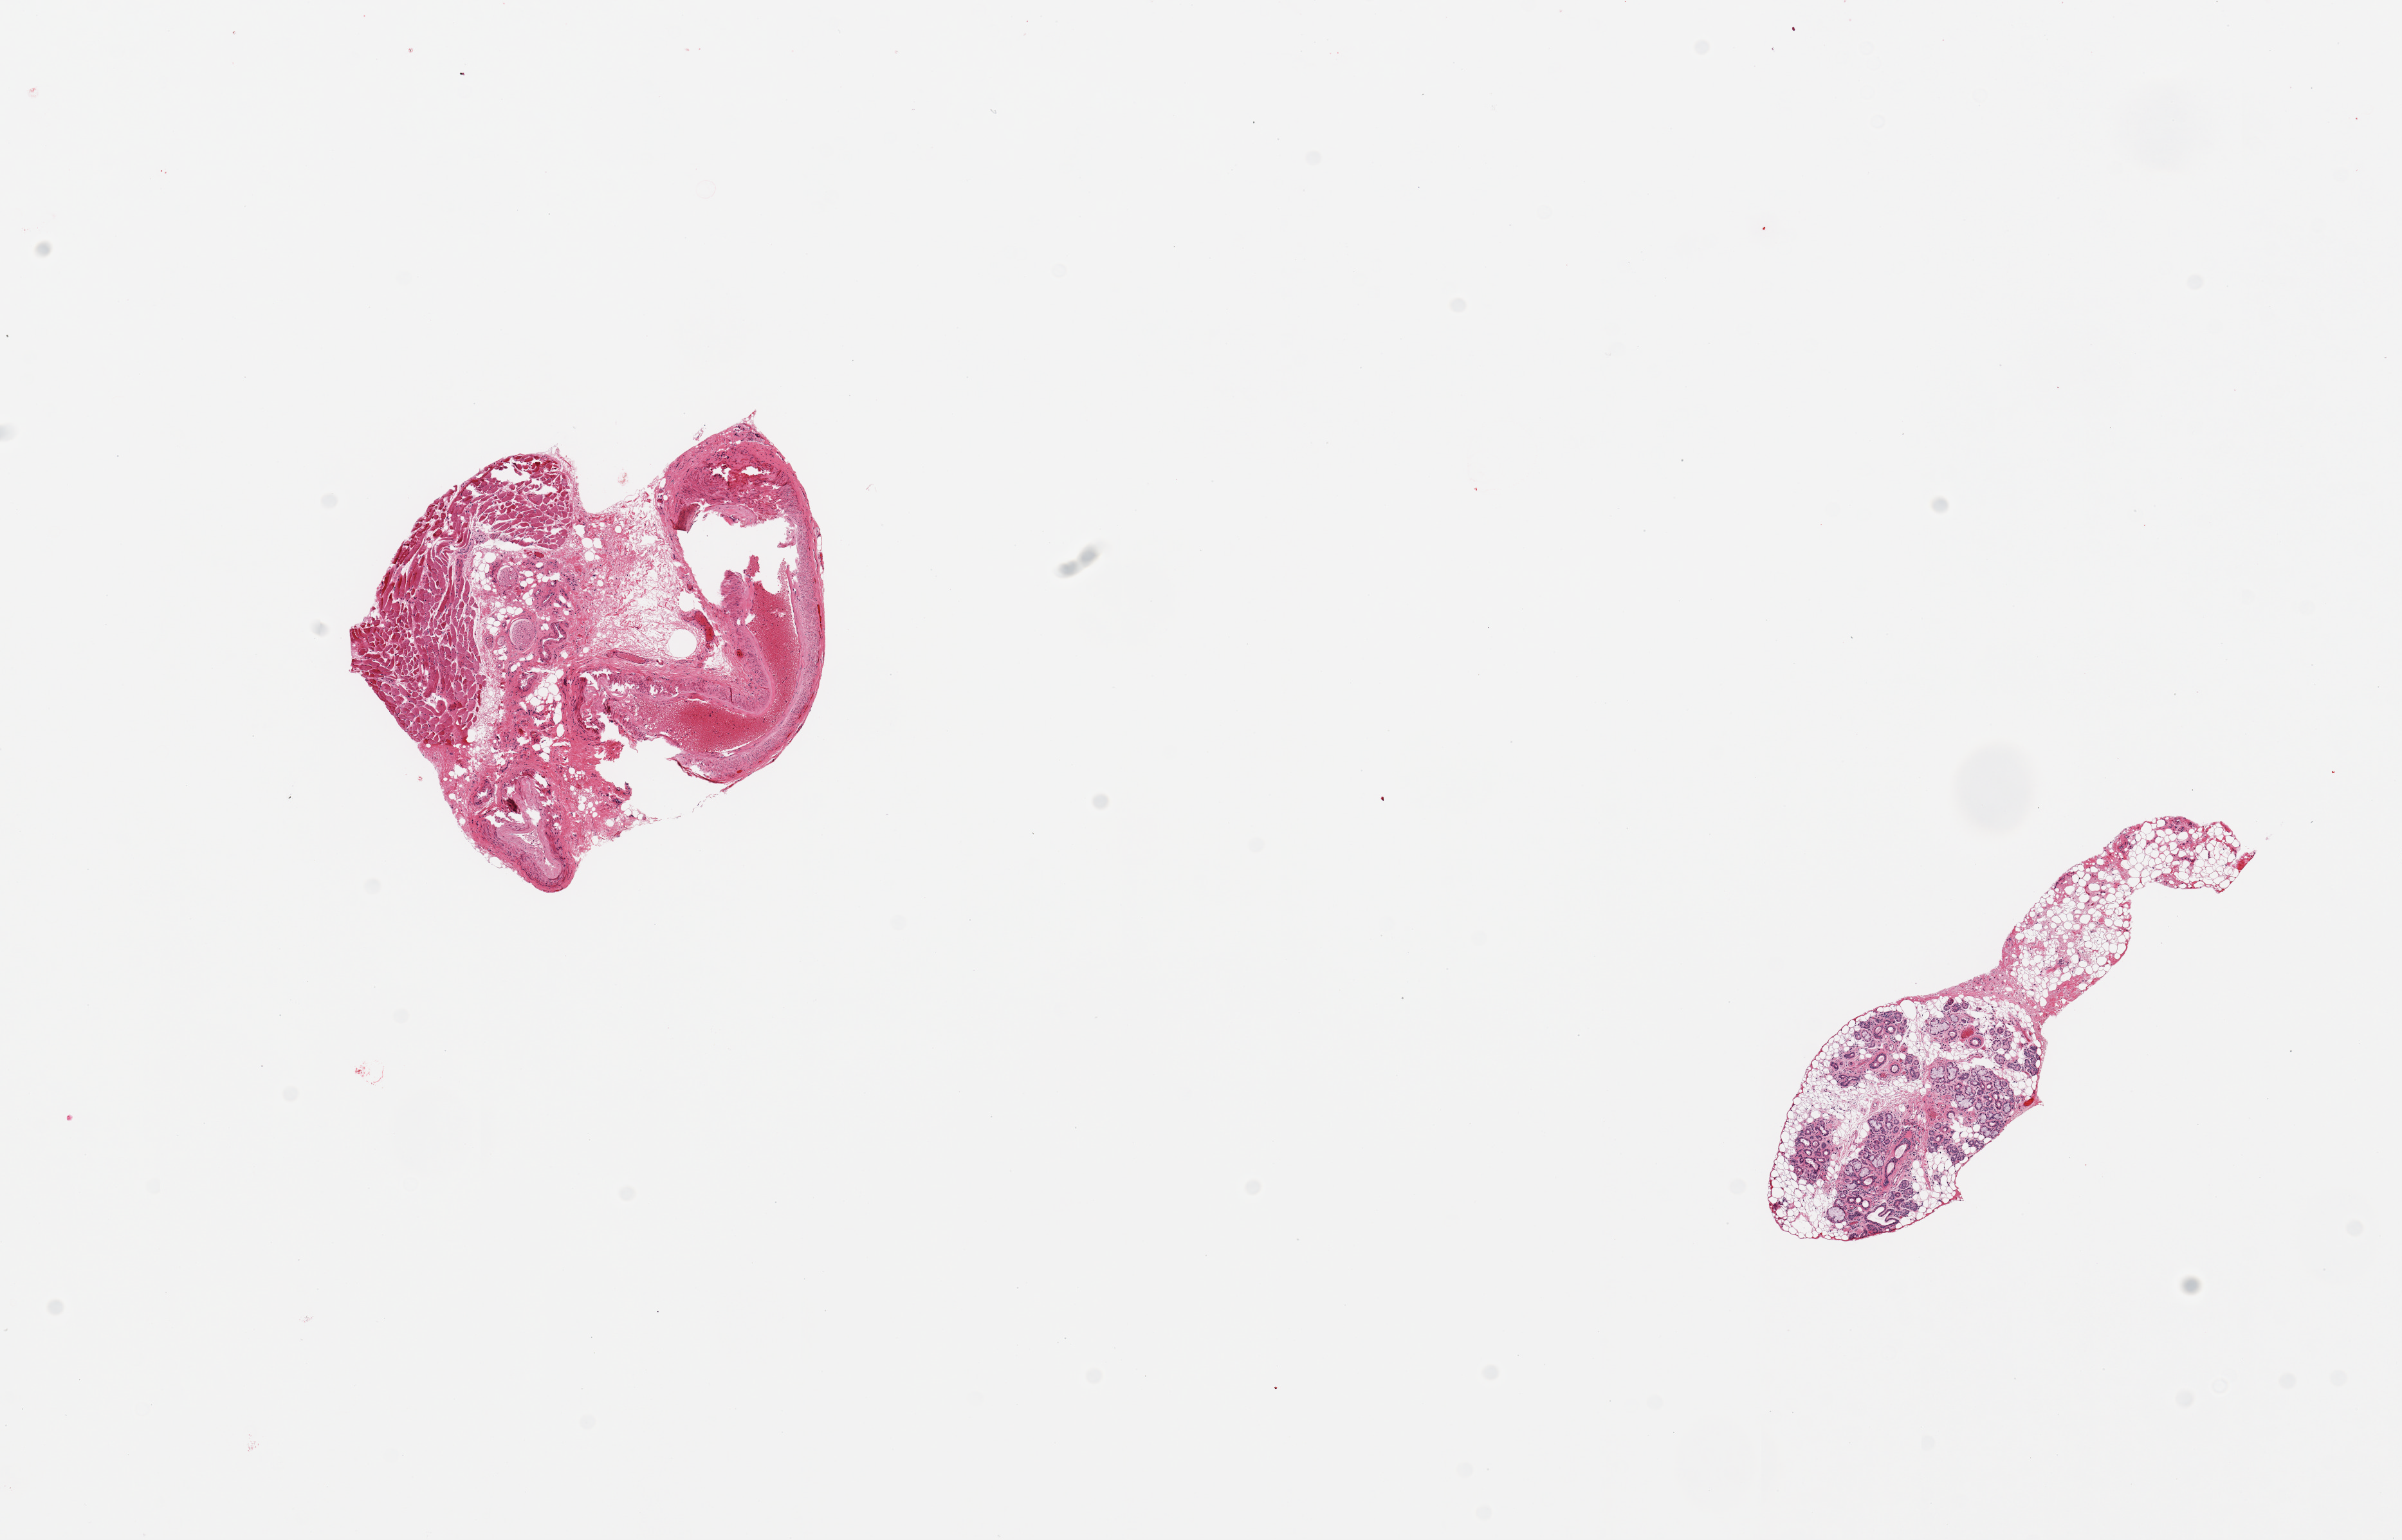
Hematoxylin and eosin (H&E) whole-slide image — a low-resolution overview of the entire scanned area, about 14.8 x 9.5 mm (from a 20x scan); PAXgene-fixed, paraffin-embedded tissue; section of minor salivary gland (target tissue); tissue donor sample. Donor: male.
Reviewer comment on this tissue sample: 2 pieces, single 1.7mm nodule of glandular tissue, rest is connect tissue elements/muscle.